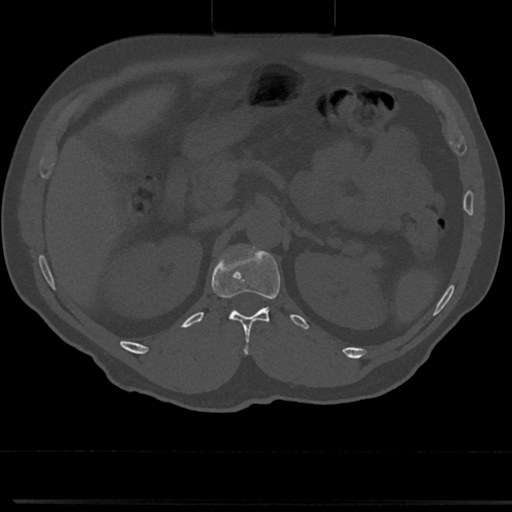
CT including the spine, one axial slice; reconstruction kernel Br40s/3; 120 kVp; bone window (W 1800 / L 400 HU); 512 × 512 image matrix, field of view 355 × 355 mm. Patient: male, 61 years. From the clinical record (not read from this slice): primary cancer: prostate.
Annotated regions visible in this slice (semi-automatic segmentation, software-assisted and operator-edited):
- T12 vertebra: bounding box (x1, y1, x2, y2) in pixels: (217, 264, 282, 357)